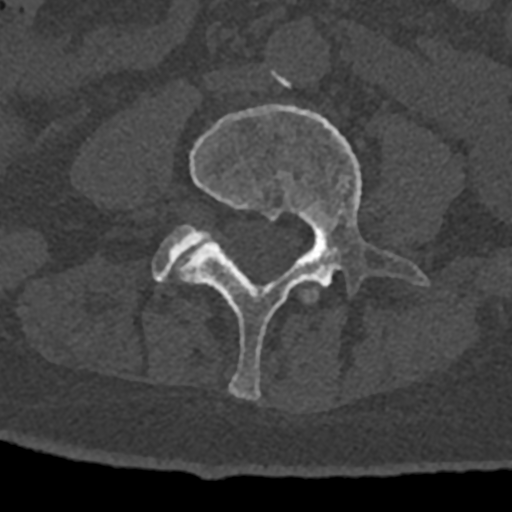
CT including the spine, one axial slice. Position 253 of 797 along the scan axis. 120 kVp. Bone window (W 1800 / L 400 HU). 512 × 512 image matrix, field of view 160 × 160 mm. Male patient, age 74 years. Case-level facts recorded for this patient, not image findings: primary cancer: renal.
Annotated regions visible in this slice (semi-automatically segmented with operator editing):
- L3 vertebra: box from (x=303, y=289) to (x=318, y=302) px
- L4 vertebra: (x=176, y=105)–(x=429, y=400)
- L5 vertebra: (x=152, y=224)–(x=210, y=283)